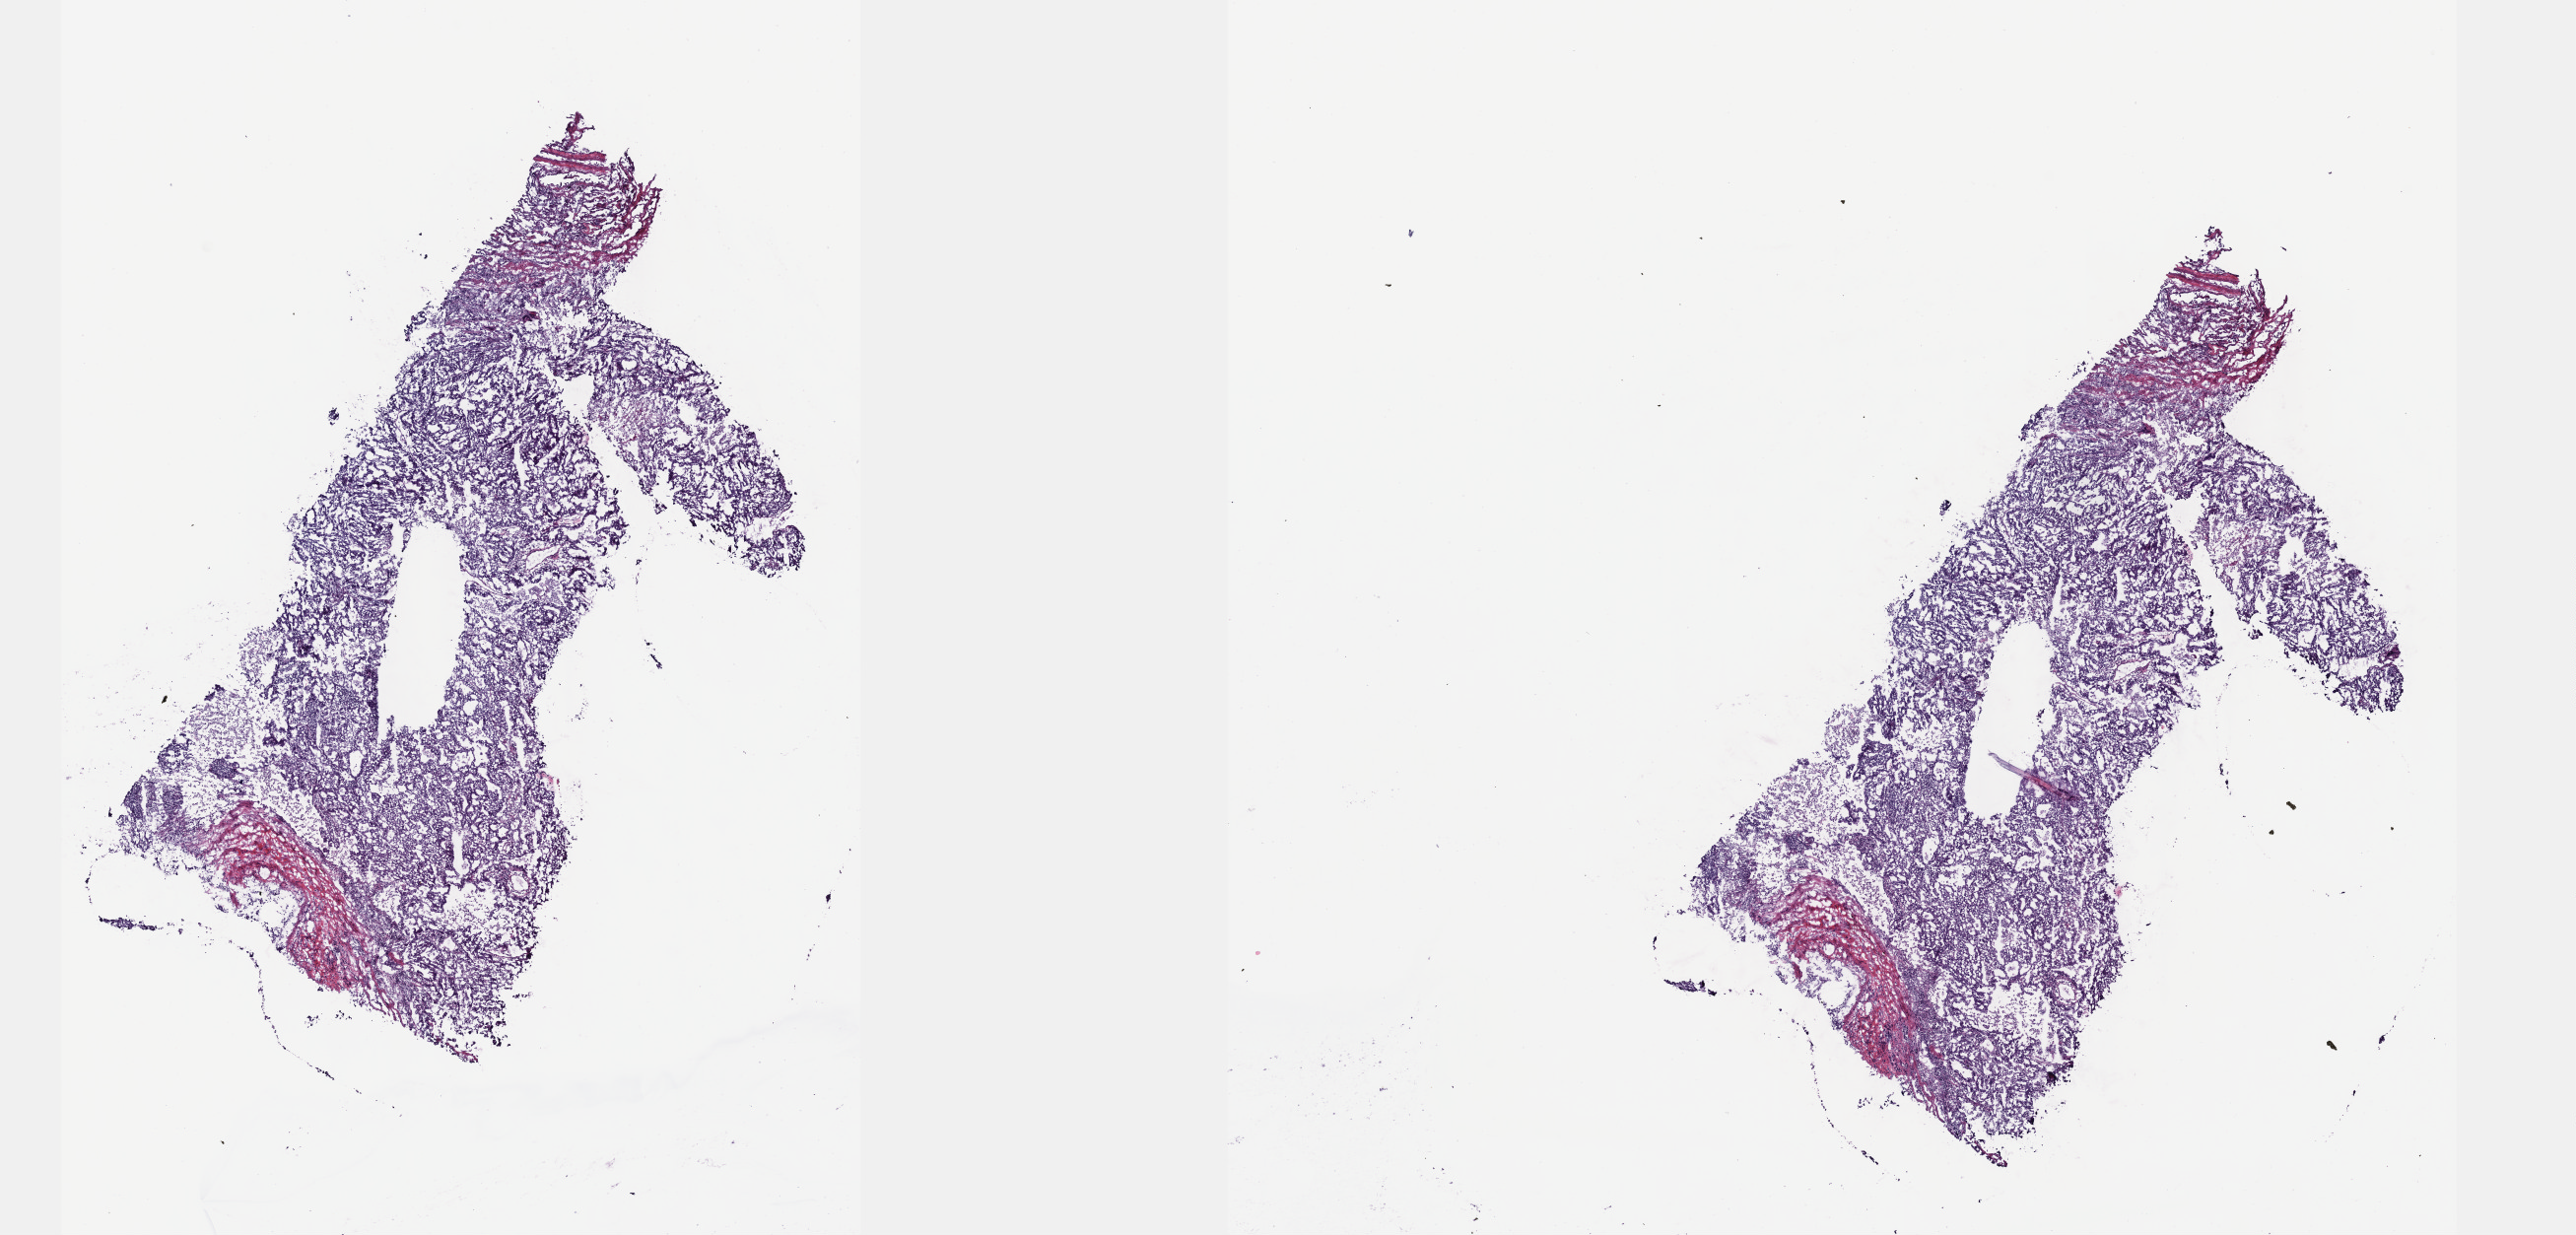
Whole-slide histology image, Hematoxylin and eosin (H&E) stained, a low-resolution overview of the entire scanned area, about 21.1 x 10.1 mm (from a 40x scan). Frozen section. Primary tumour sample from the lung. Male, age 64 years at initial diagnosis. Slide review estimates, as recorded: tumour cells 80%, tumour nuclei 80%, normal cells 0%, stromal cells 19%, necrosis 1%. Infiltration values recorded for this section: lymphocyte infiltration 2%, monocyte infiltration 5%, neutrophil infiltration 3%.
Pathologic diagnosis: Acinar cell carcinoma (lower lobe, lung). AJCC pathologic stage: IB (6th edition).